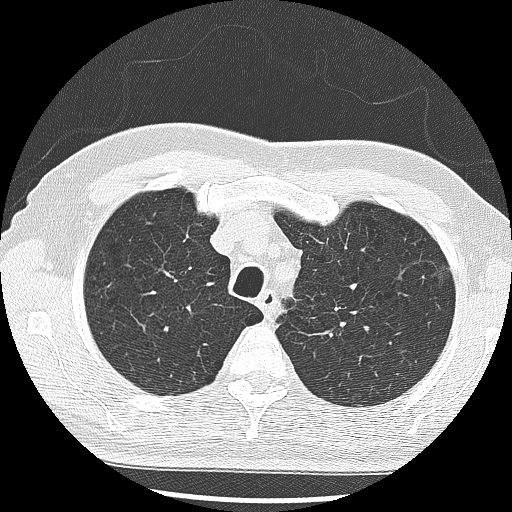
Low-dose screening chest CT, one axial slice; position 225 of 285 along the scan axis; lung window (W 1500 / L -600 HU); 2.5 mm slice thickness; 512 × 512 image matrix, field of view 340 × 340 mm.
Structures marked on this image (manually delineated by an expert):
- lesion 1 (tumor, upper lobe of left lung): bounding box [x1, y1, x2, y2] px = [433, 266, 450, 278]